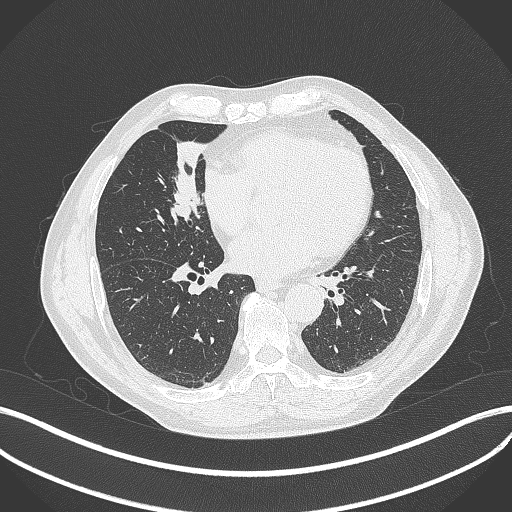
Chest CT, one axial slice. Position 165 of 429 along the scan axis. Reconstruction kernel B70f. 120 kVp. Lung window (W 1500 / L -600 HU). 512 × 512 image matrix, field of view 400 × 400 mm. Patient: male, 61 years. From the clinical record (not read from this slice): clinical TNM (as recorded): T2b N1 M0.
Outlined on this slice (rectangle marked by the reading radiologist):
- lung tumour (recorded histology: squamous cell carcinoma): bounding box [x1, y1, x2, y2] px = [165, 166, 209, 232]